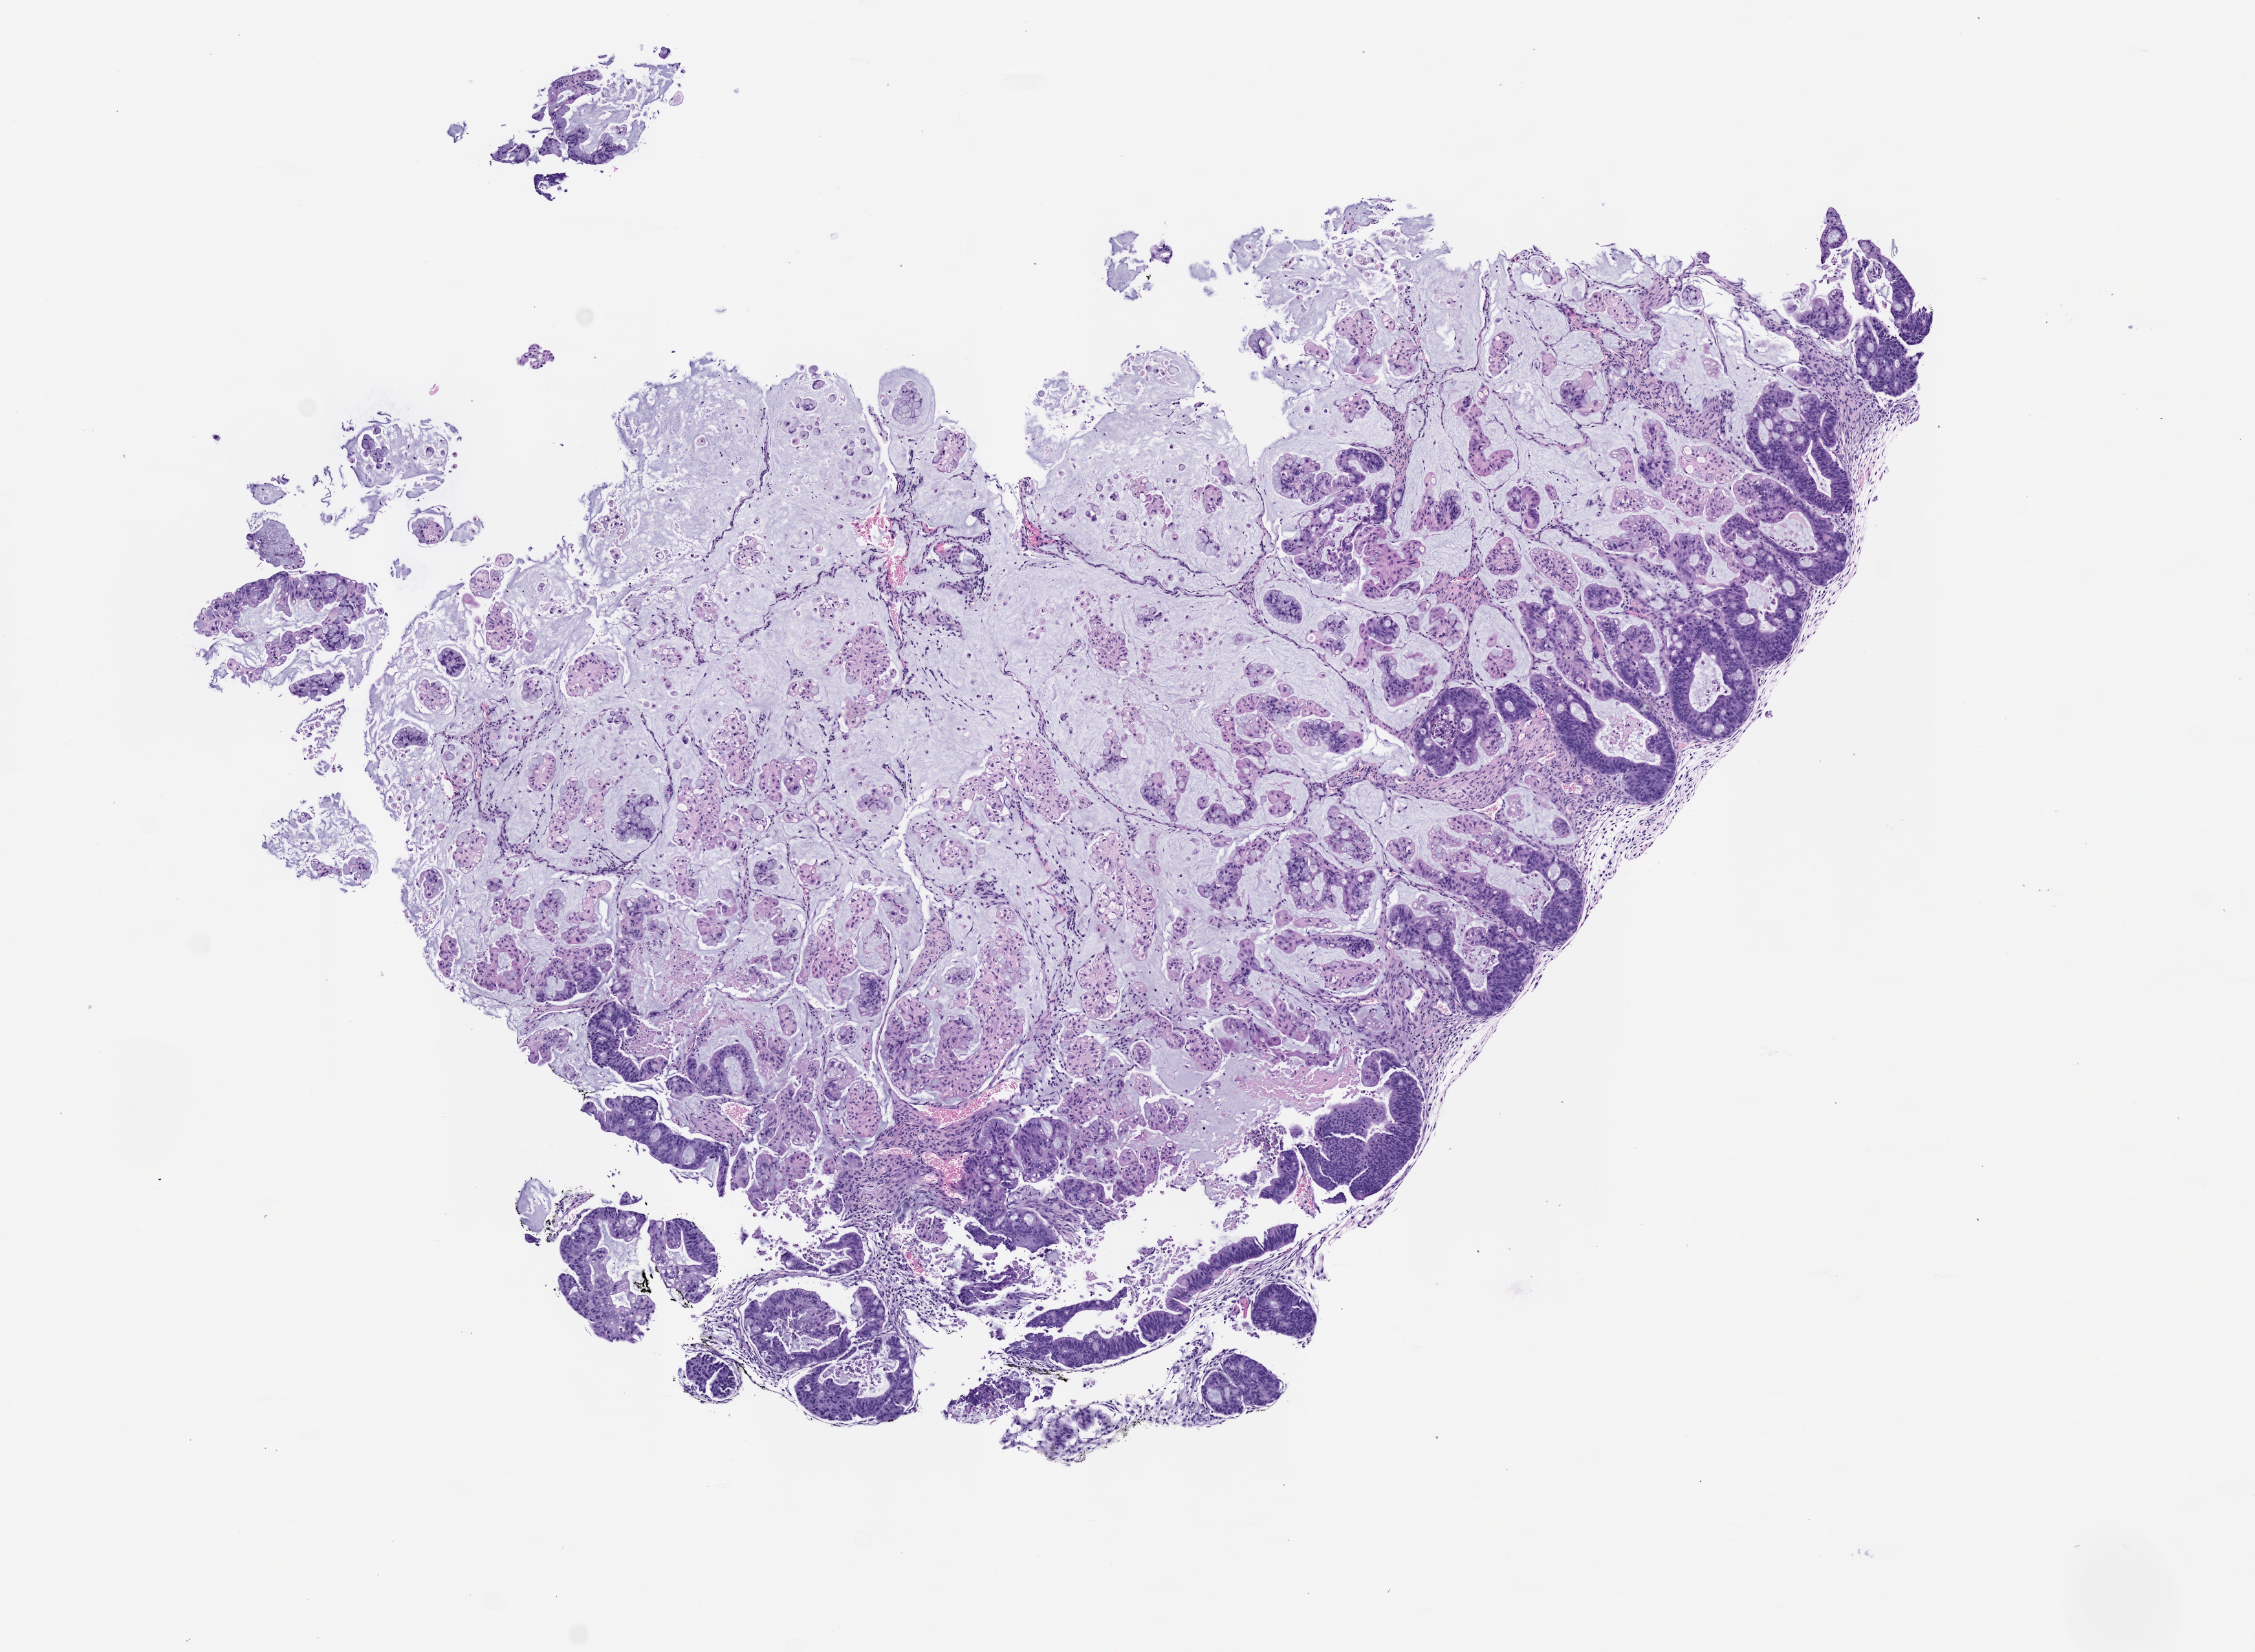
Whole-slide image, hematoxylin and eosin (H&E): patient-derived xenograft (human tumor grown in a mouse), passage 1 — low-resolution overview of the scanned area, about 7.0 x 5.1 mm. Formalin-fixed, paraffin-embedded (FFPE) tissue. Originating tumor site category: colon.
- originating patient diagnosis: Colon Adenocarcinoma